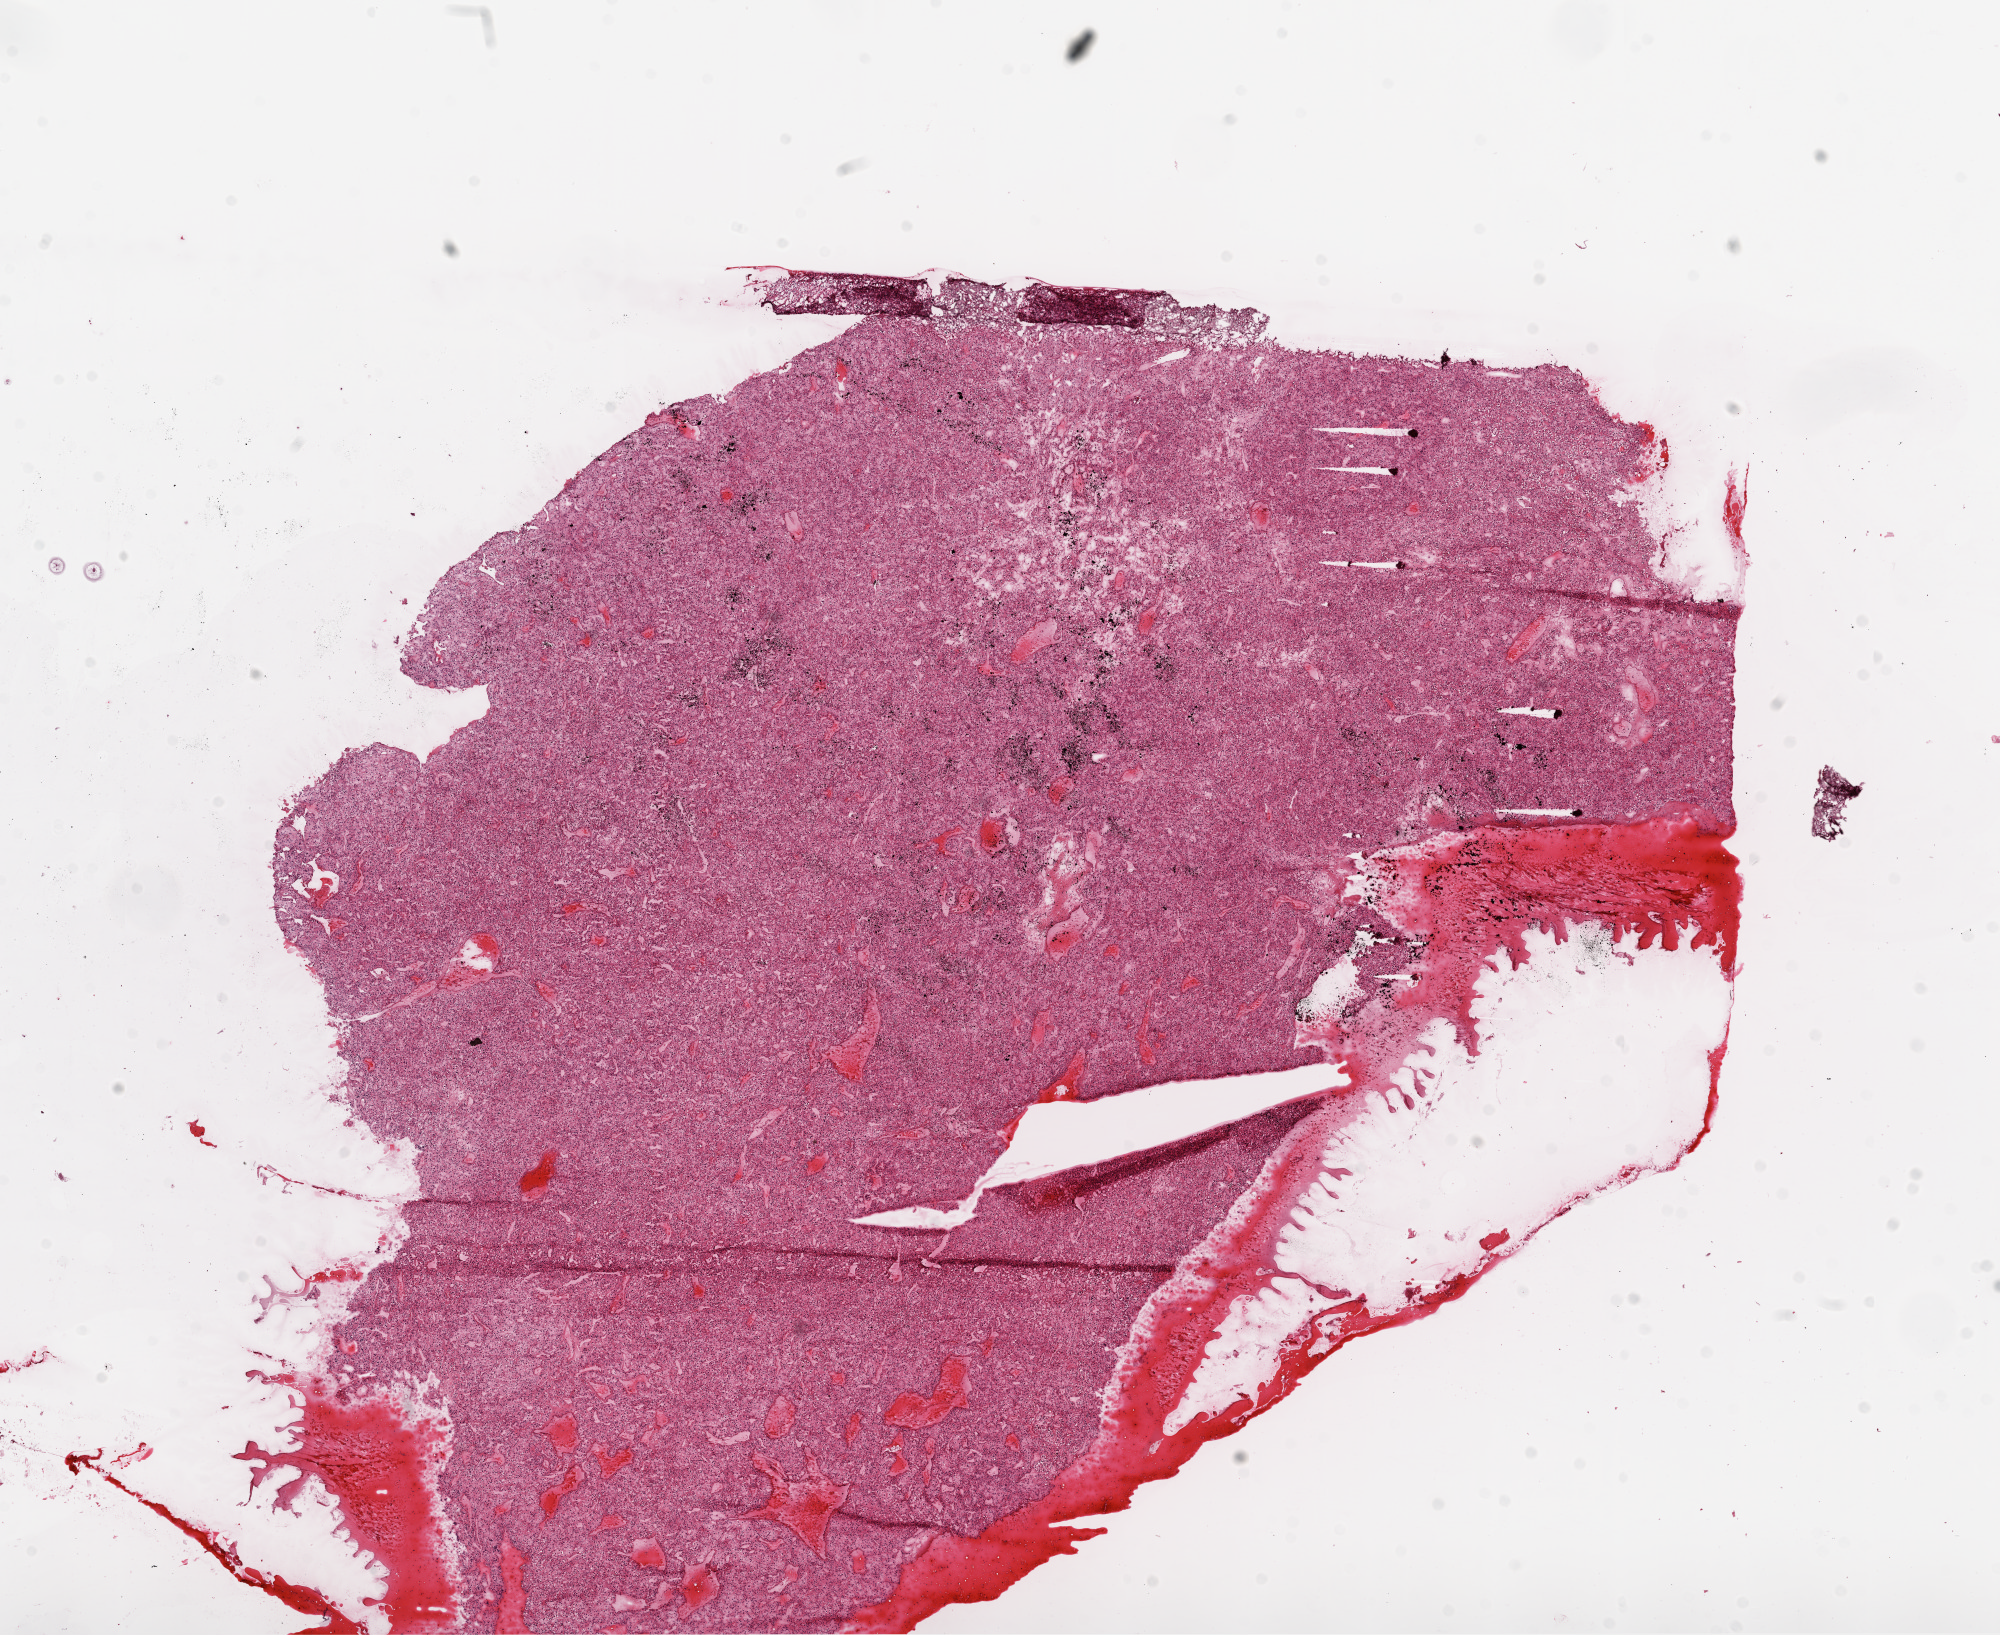
H&E-stained whole-slide image — whole scanned area (about 16.0 x 13.1 mm) shown as a low-resolution overview; frozen section from the top of the tissue portion; sample: primary tumour, kidney. Patient: male, age at initial diagnosis 47 years. Histologic grade: G3 (poorly differentiated). Composition of this section per pathologist review: tumour cells 90%, tumour nuclei 85%, normal cells 0%, stromal cells 10%, necrosis 0%.
Histologic diagnosis: Clear cell adenocarcinoma, NOS. AJCC pathologic stage: III.